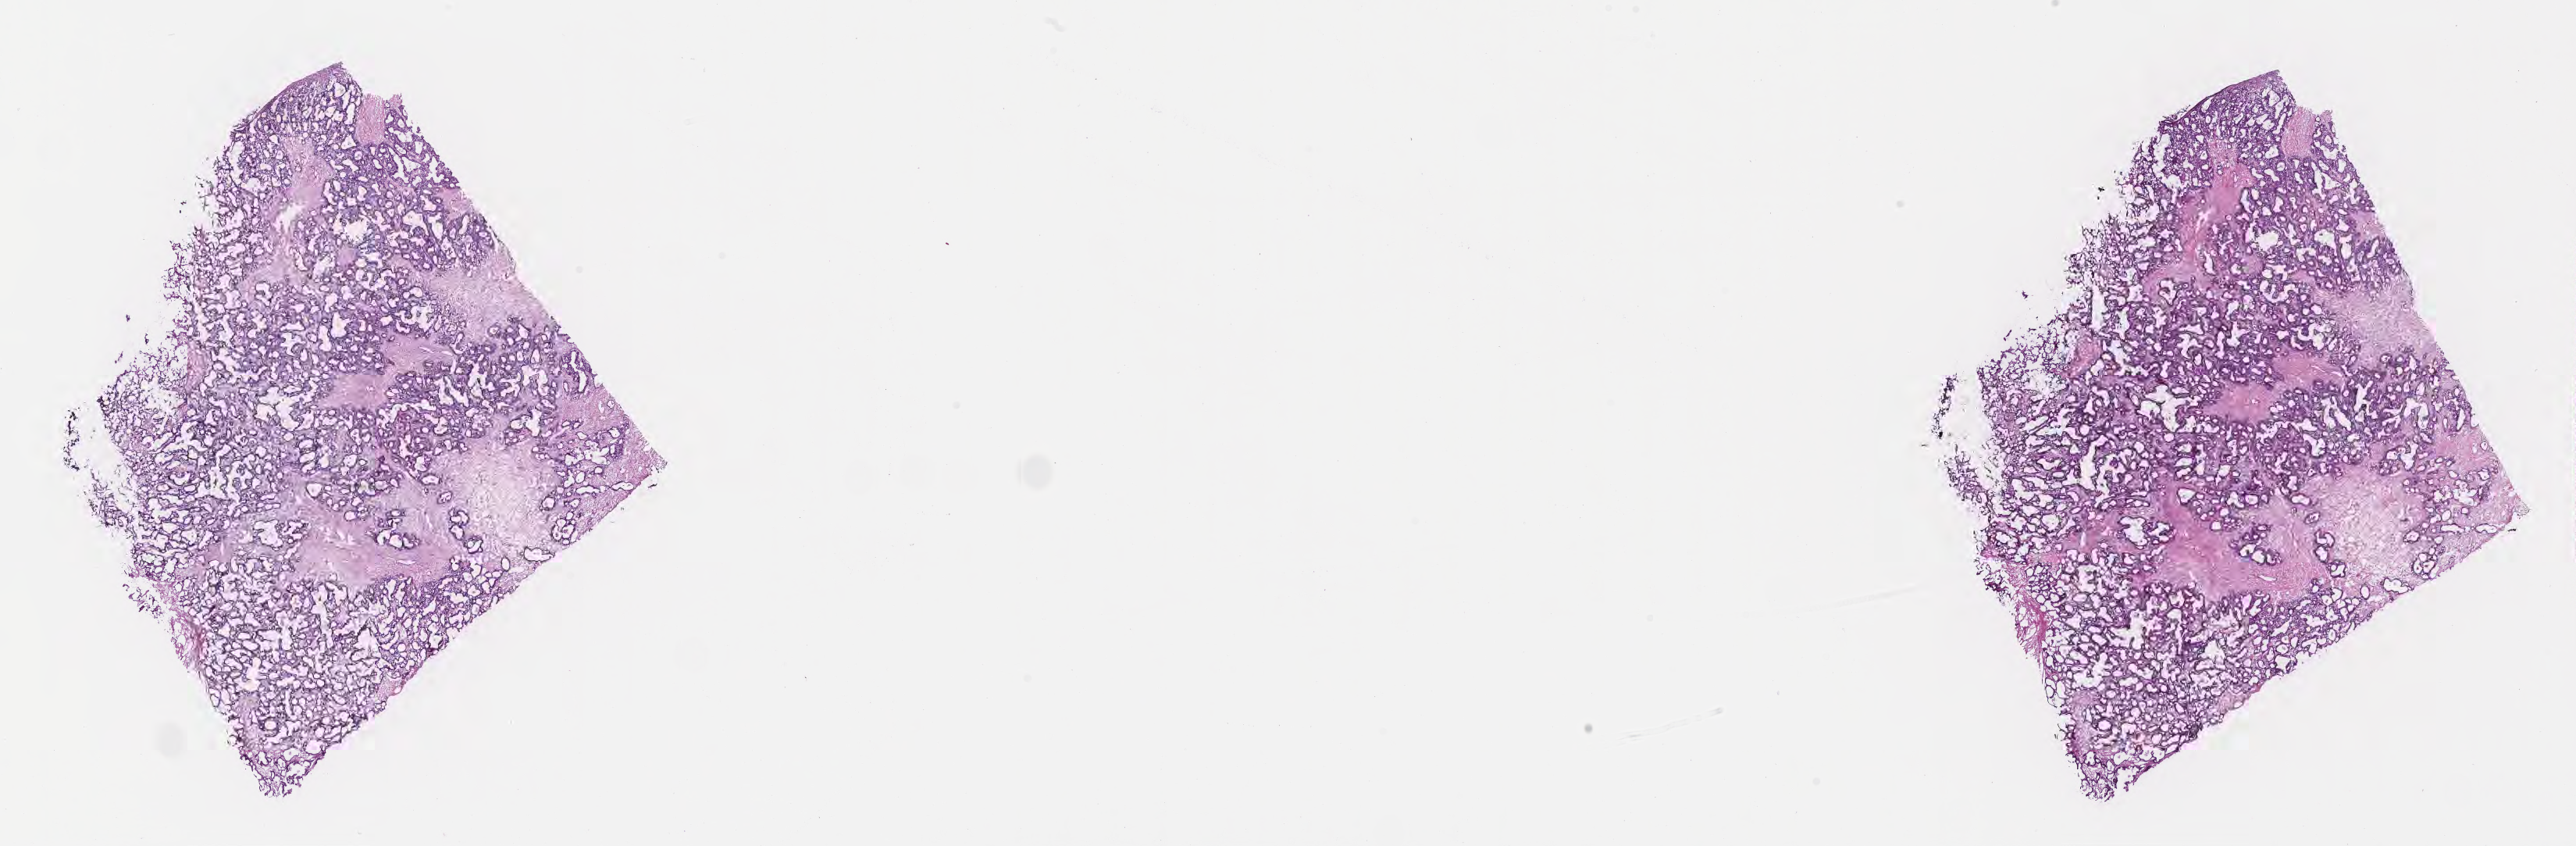
Digitized H&E-stained section — a low-resolution overview of the entire scanned area, about 26.7 x 8.8 mm, frozen section (tissue freezing medium), metastatic tumor tissue, resected from liver. Male, age 61 years at initial diagnosis. Slide review estimates, as recorded: tumor cells 85%, tumor nuclei 85%, stromal cells 15%, necrosis 0%, normal cells 0%. Inflammatory infiltration, as recorded: lymphocyte infiltration 5%, monocyte infiltration 2%, neutrophil infiltration 3%.
Patient diagnosis (primary): Adenocarcinoma, metastatic, NOS.